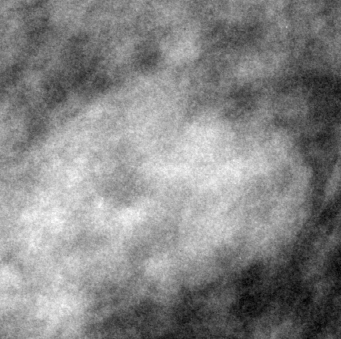
Crop from a digitized film mammogram around one marked abnormality; right breast; MLO view; BI-RADS breast density category 3 (scale 1–4).
Finding: mass, shape oval, margins circumscribed; BI-RADS assessment category 3; subtlety rating 3 on a 1 (subtle) to 5 (obvious) scale; pathology result (as recorded, not read from the image): benign.